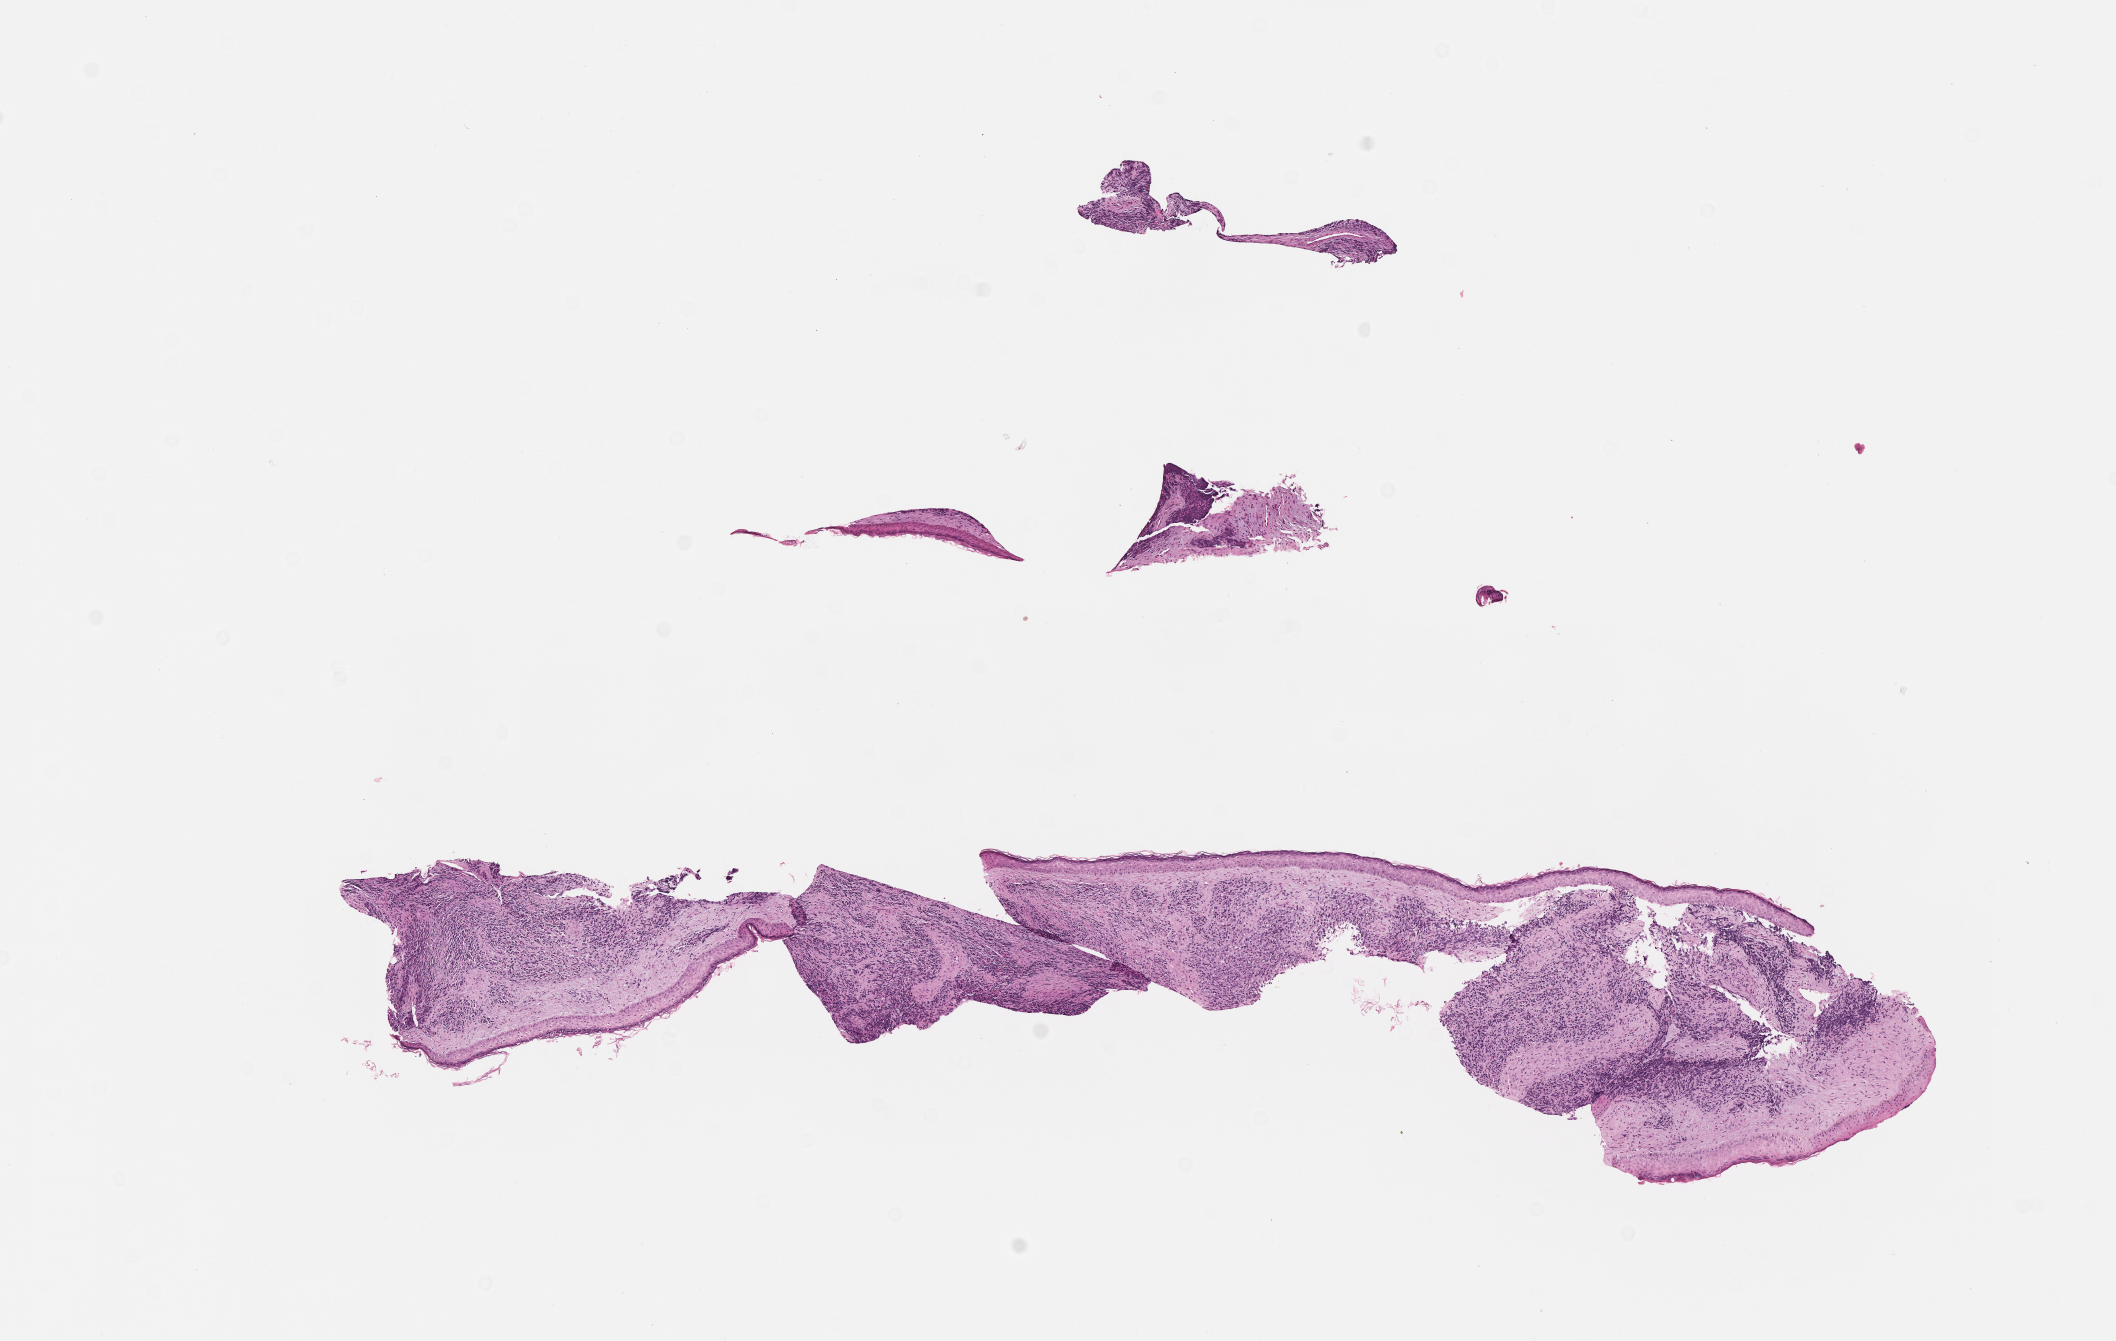
Digitized haematoxylin and eosin-stained section of tumor tissue — whole scanned area (about 8.6 x 5.4 mm) shown as a low-resolution overview. Formalin-fixed, paraffin-embedded (FFPE) tissue. Site: soft tissue, ear-left. Male patient, age at diagnosis 1.8 years.
Diagnosis: rhabdomyosarcoma; histological classification: embryonal rhabdomyosarcoma. Stage (as recorded): 3. Metastatic status at presentation (as recorded): non-metastatic.